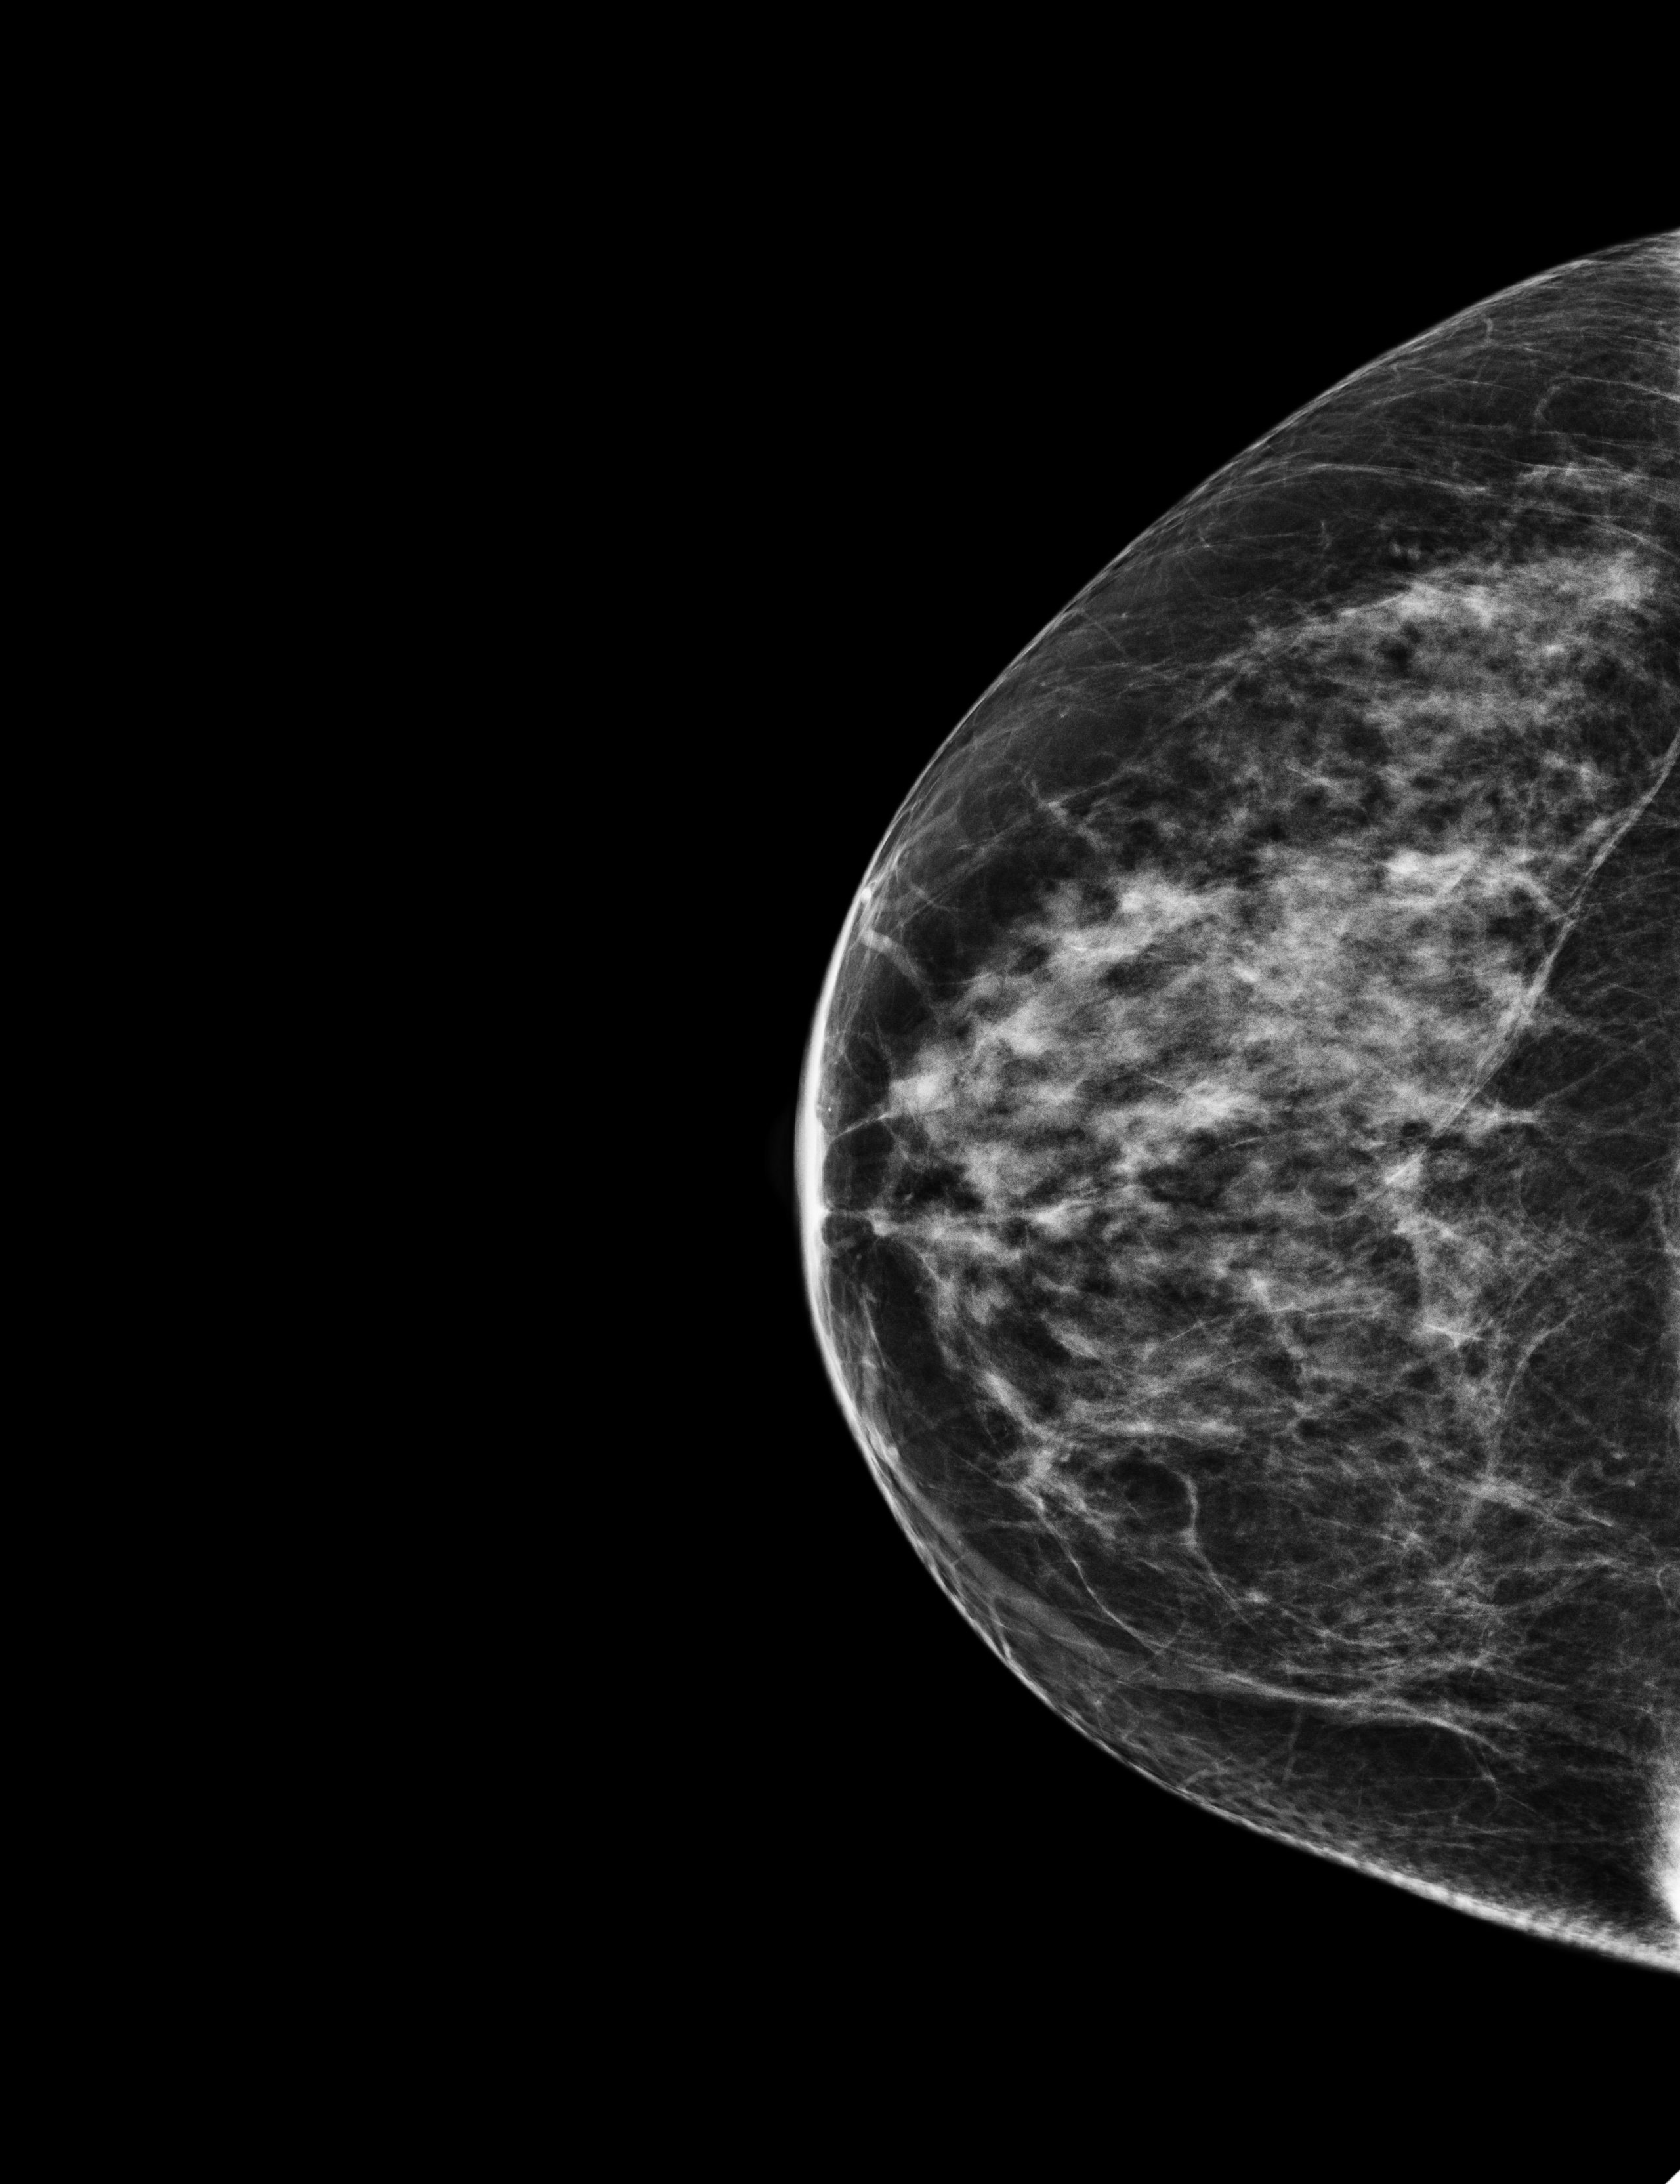
Screening examination; system: Selenia Dimensions.
Image type: full-field digital mammogram. Breast: right. Projection: CC view.